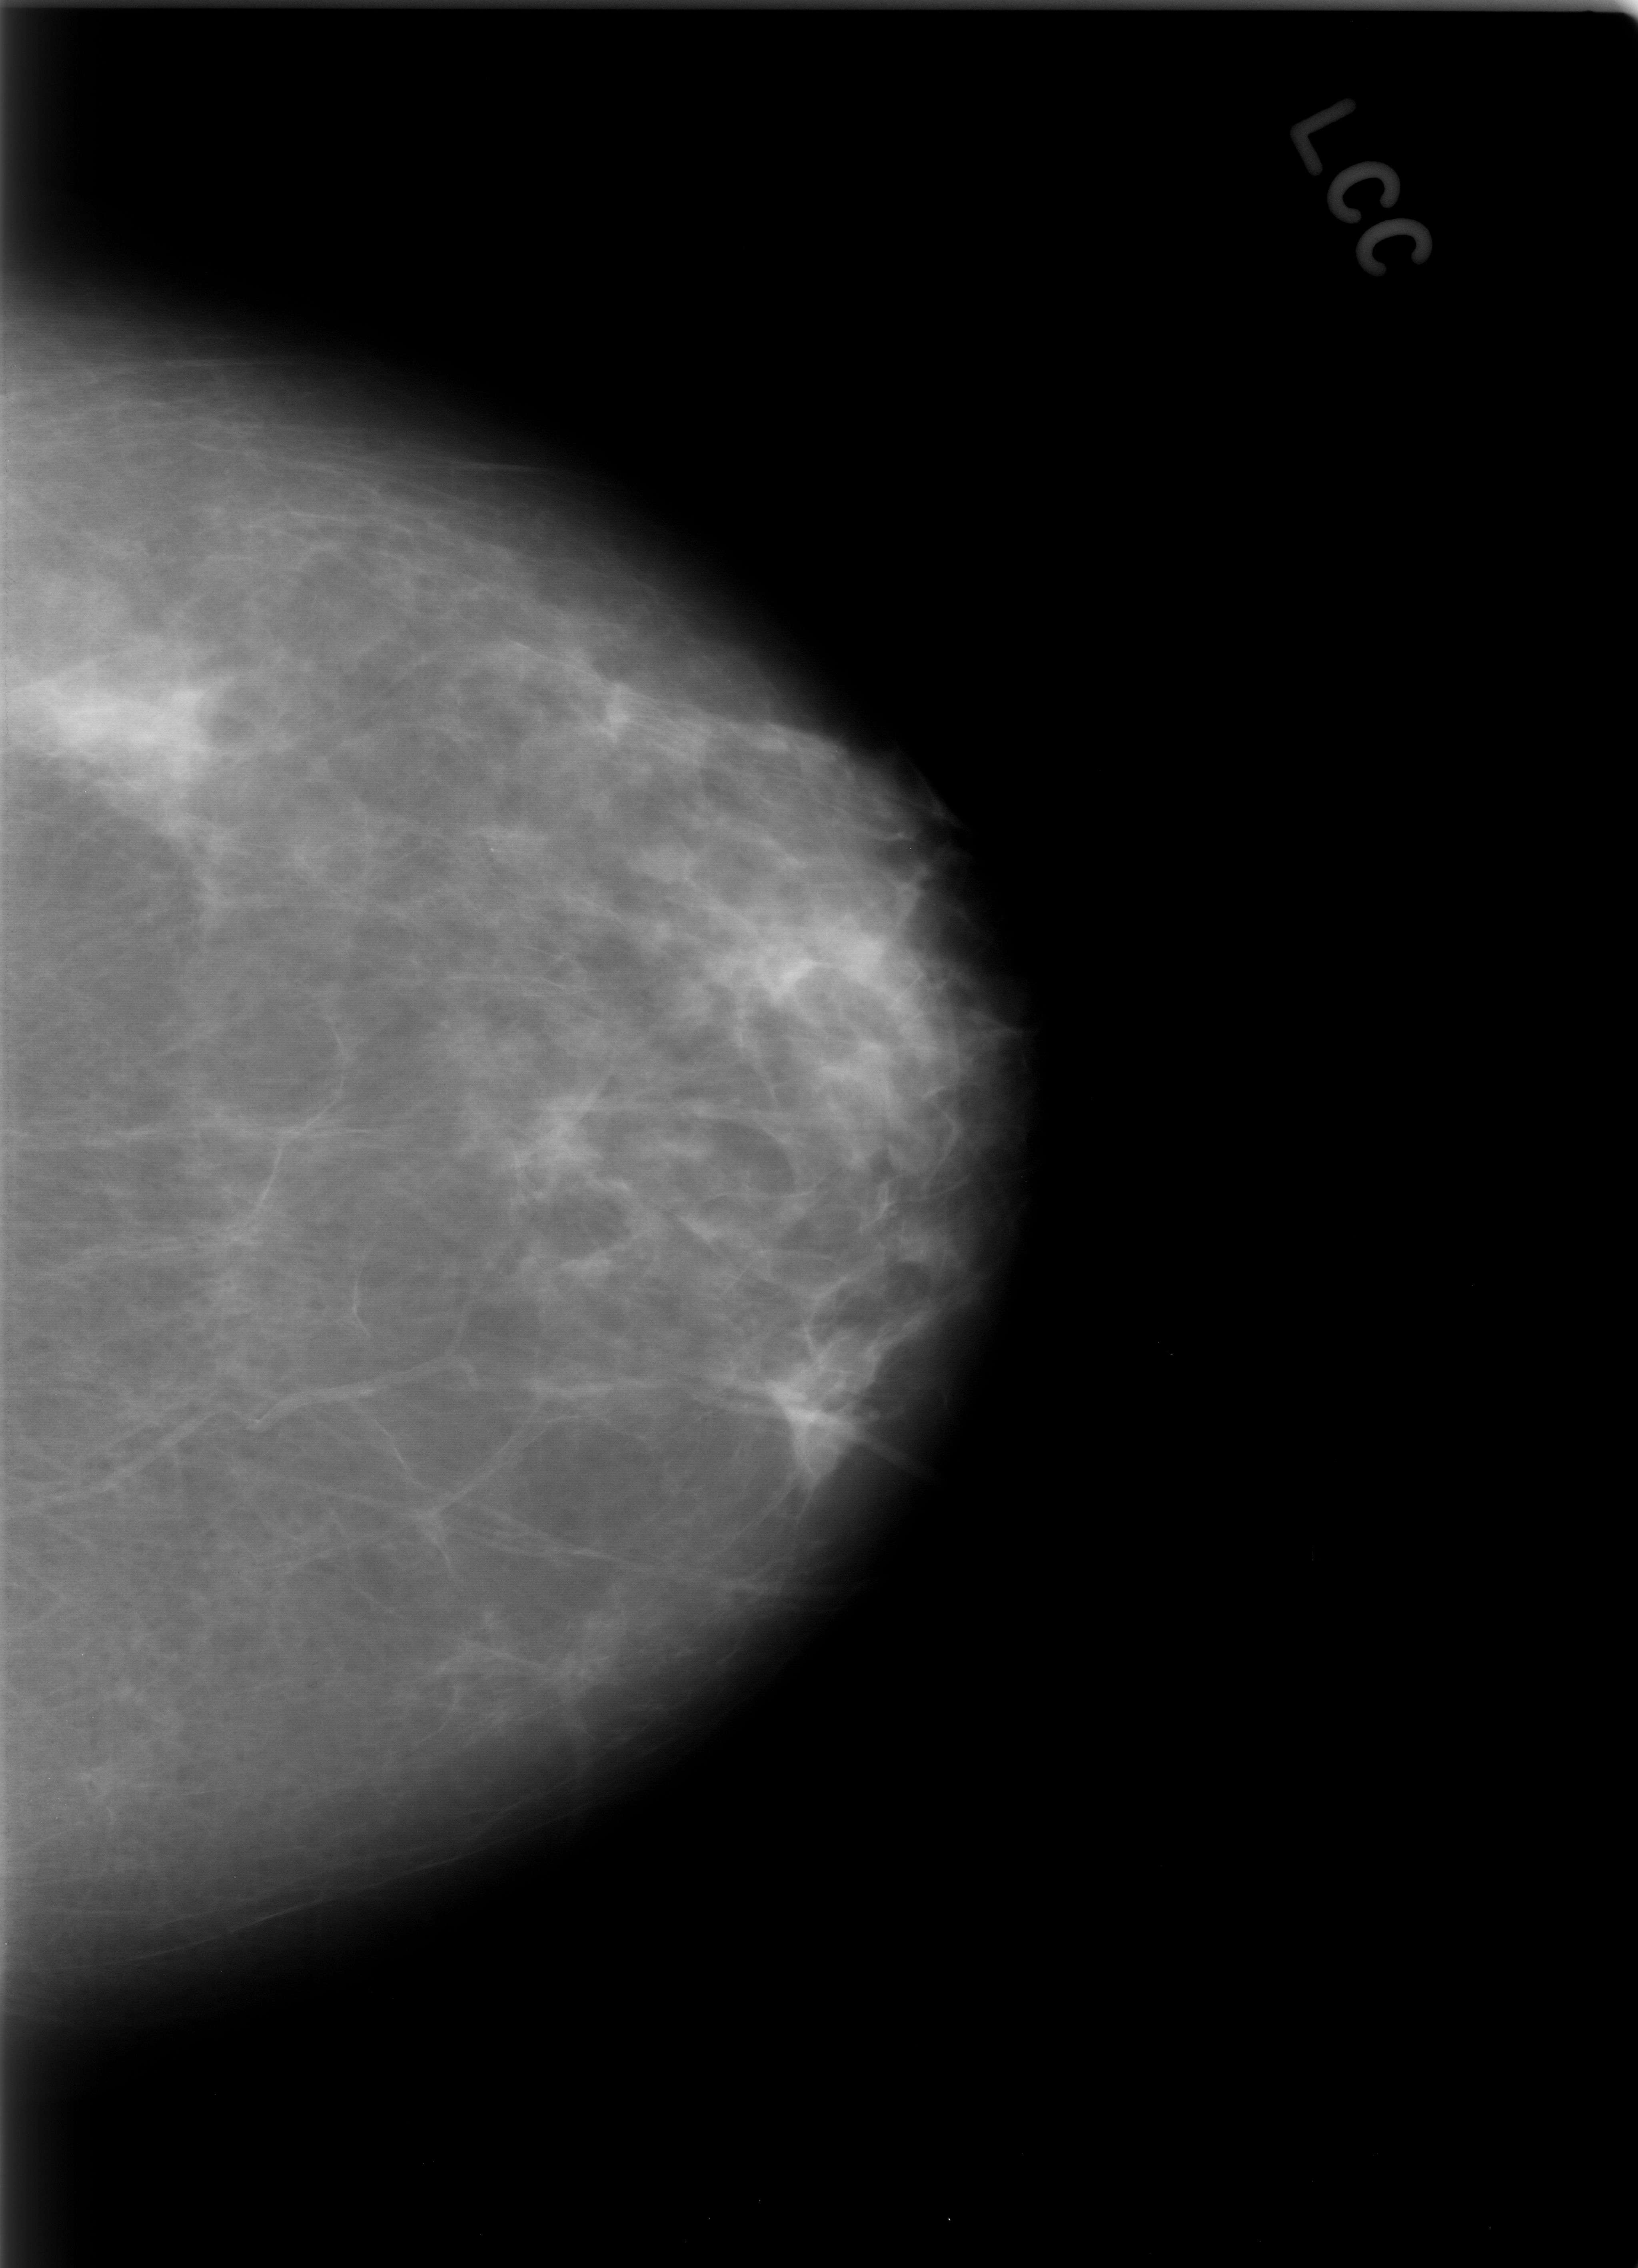
Scanned film-screen mammogram. Left breast. CC view. Breast composition: scattered fibroglandular densities (BI-RADS density category 2 of 4). 1638 × 2268 image matrix.
Marked abnormalities (boxes around the expert regions of interest):
- calcifications, morphology pleomorphic, distribution clustered; BI-RADS assessment category 4; pathology (as recorded): benign: box from (x=108, y=405) to (x=247, y=513) px